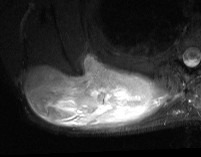
MRI of an extremity soft-tissue mass, one axial slice. Slice 29 of 74 in the series (ordered by position). STIR. MR volume resampled by the dataset authors to the PET/CT grid (not the native acquisition matrix). 3.27 mm slice thickness. 201 × 157 image matrix, field of view 196 × 153 mm. Male patient. From the clinical record (not read from this slice): histological type: pleiomorphic spindle cell undifferentiated; grade: high; site of the primary tumour: right parascapusular.
Outlined on this slice (expert contour drawn on MRI and transferred to this co-registered scan by the dataset authors):
- gross tumour volume including surrounding oedema: box from (x=24, y=55) to (x=173, y=131) px
- gross tumour volume (mass): (x=24, y=55)–(x=155, y=127)